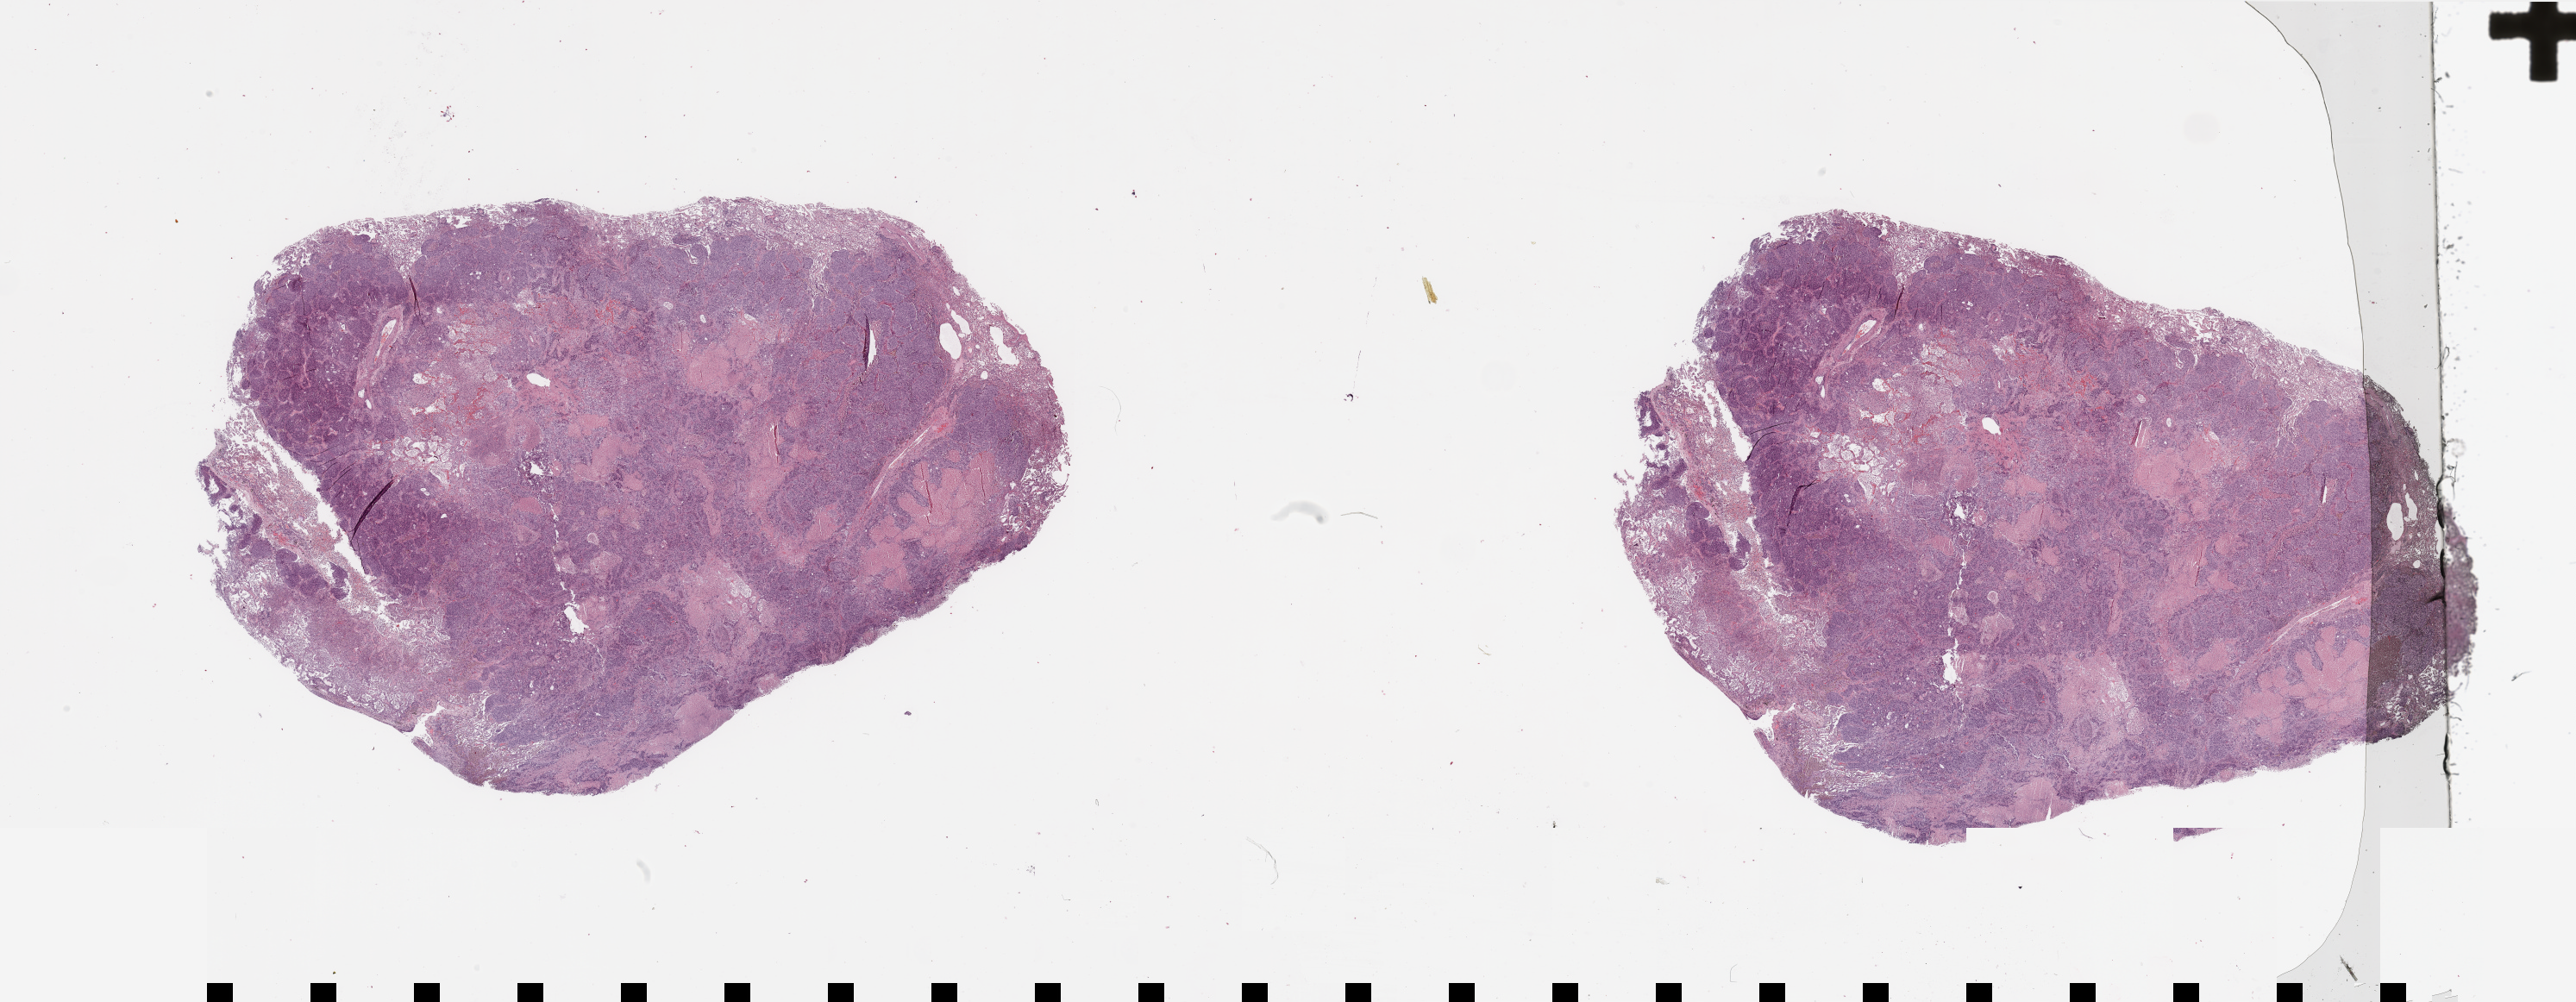
H&E-stained whole-slide image, shown as a low-resolution overview of the whole scanned area (about 47.3 x 18.4 mm, acquisition: 20x scan). Lung, tumour tissue. Patient: male, age 57 years. Histologic grade: G3 (poorly differentiated).
AJCC pathologic stage: IA. Diagnosis: Squamous cell carcinoma, NOS. Primary tumour site (as recorded): right lower lobe.